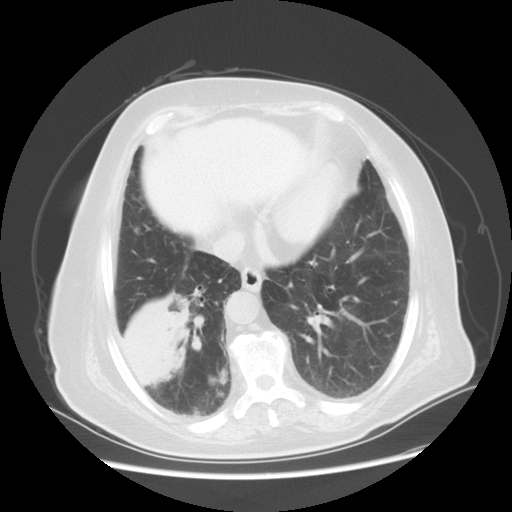
Chest CT, one axial slice. Slice 19 of 56 in the series (ordered by position). Lung window (W 1500 / L -600 HU). 512 × 512 image matrix, field of view 378 × 378 mm. Female patient, age 73 years. From the clinical record (not read from this slice): clinical TNM (as recorded): T3 N0 M0.
Annotated regions visible in this slice (bounding box drawn by a radiologist):
- lung tumour (recorded histology: adenocarcinoma): bounding box (x1, y1, x2, y2) in pixels: (112, 289, 197, 391)